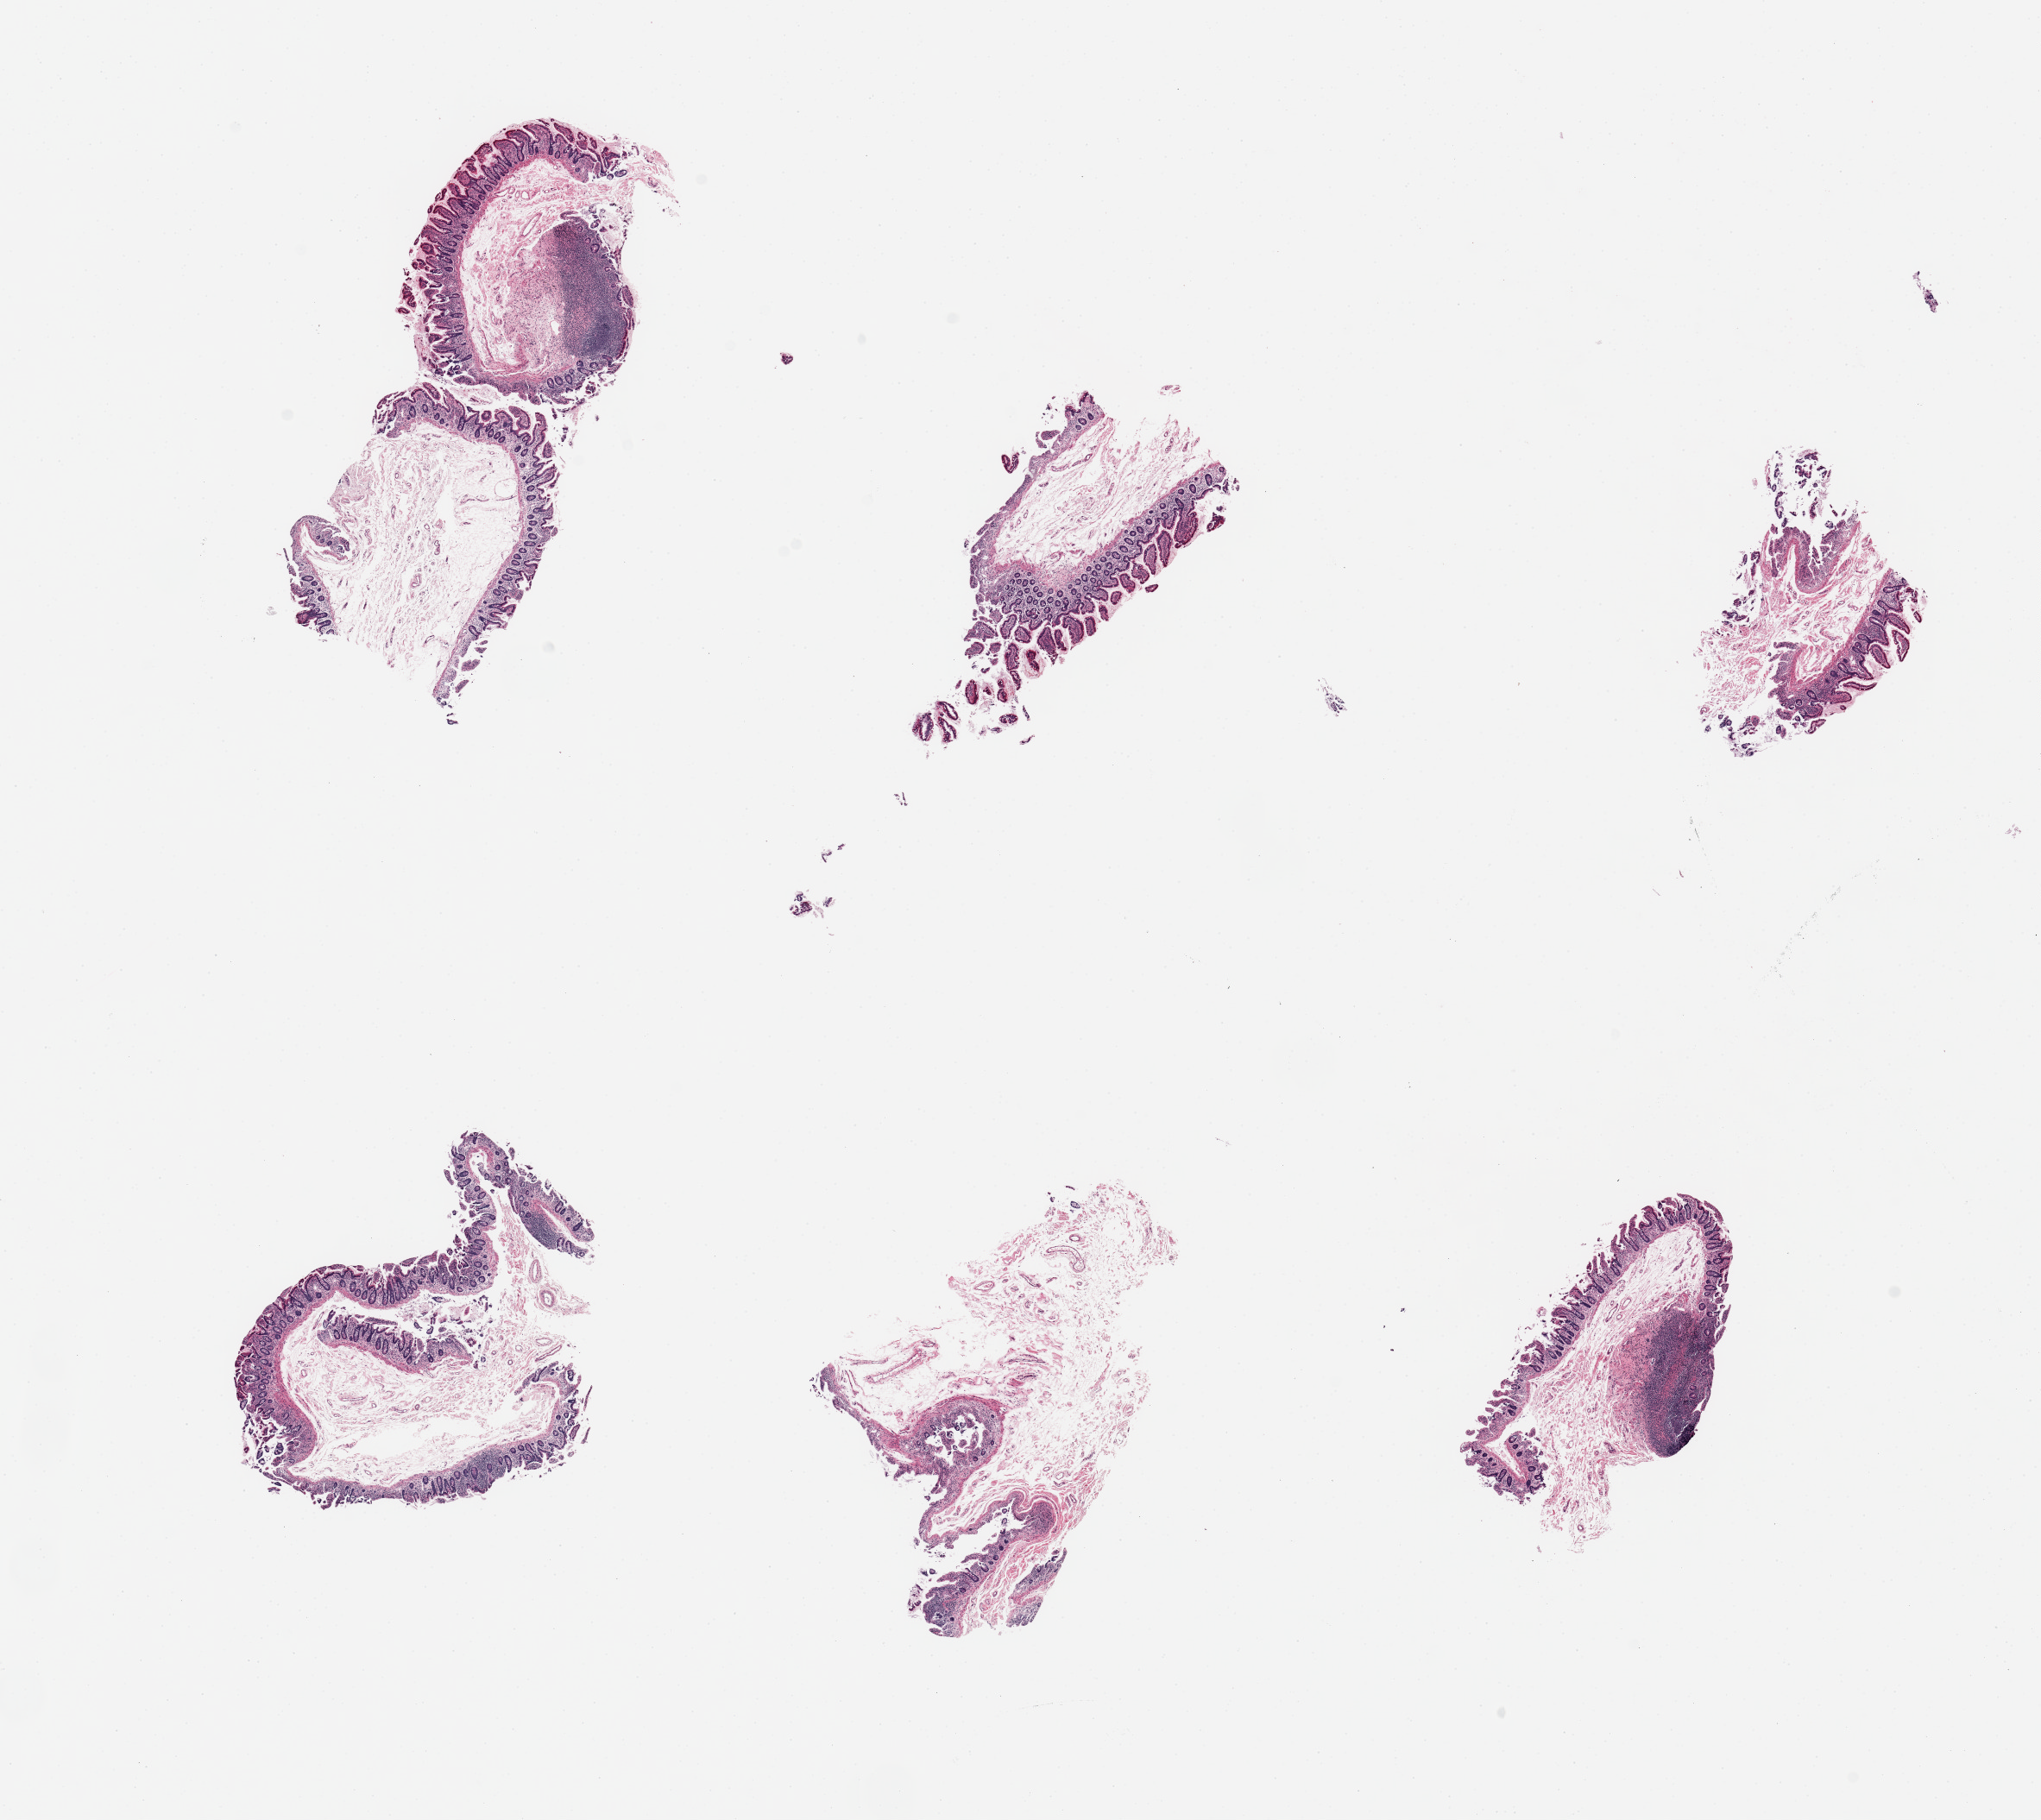
Hematoxylin and eosin (H&E) whole-slide image, shown as a low-resolution overview of the whole scanned area (about 18.7 x 16.7 mm, acquisition: 20x scan). PAXgene-fixed paraffin-embedded (PFPE) section. Section of ileum (target tissue). Tissue donor sample. Donor sex: female.
Review note (as recorded): 6 pieces; only 2 lymphoid nodules.